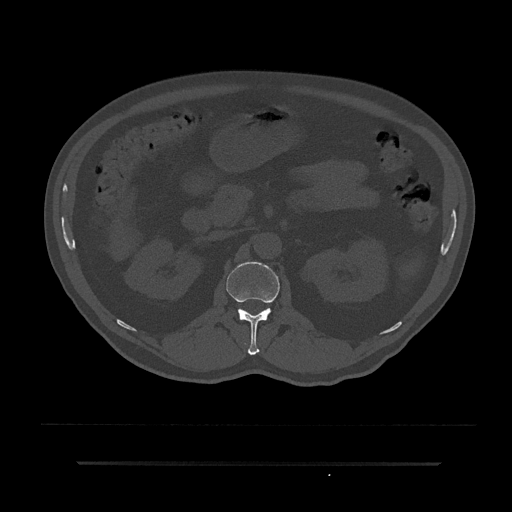
CT including the spine, one axial slice. Slice 135 of 797 in the series (ordered by position). Reconstruction kernel Br40s/3. Bone window (W 1800 / L 400 HU). 0.5 mm slice thickness. 512 × 512 image matrix. Patient: male, 59 years. Case-level facts recorded for this patient, not image findings: primary cancer: bile ducts; vertebrae with lytic lesions (as recorded): T10.
Outlined on this slice (semi-automatic segmentation, software-assisted and operator-edited):
- L1 vertebra: bounding box (x1, y1, x2, y2) in pixels: (226, 262, 280, 355)